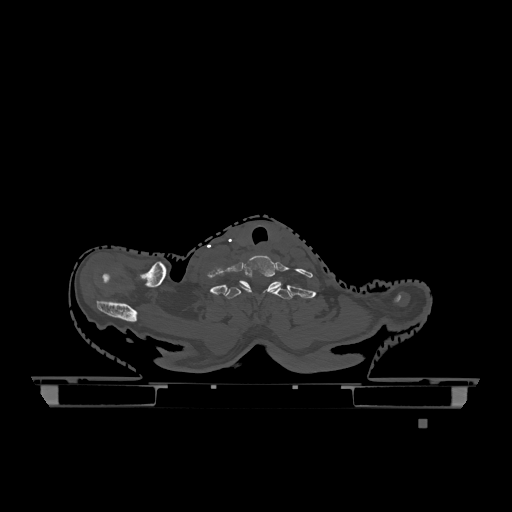
CT including the spine, one axial slice. Slice 1014 of 1317 in the series (ordered by position). Bone window (W 1800 / L 400 HU). 0.5 mm slice thickness. 512 × 512 image matrix. Female patient, age 74 years. From the clinical record (not read from this slice): primary cancer: lung; vertebrae with lytic lesions (as recorded): T1, T4, T5, T6, L4, L5.
Annotated regions visible in this slice (semi-automatic segmentation, software-assisted and operator-edited):
- T1 vertebra: bounding box (x1, y1, x2, y2) in pixels: (223, 281, 291, 299)